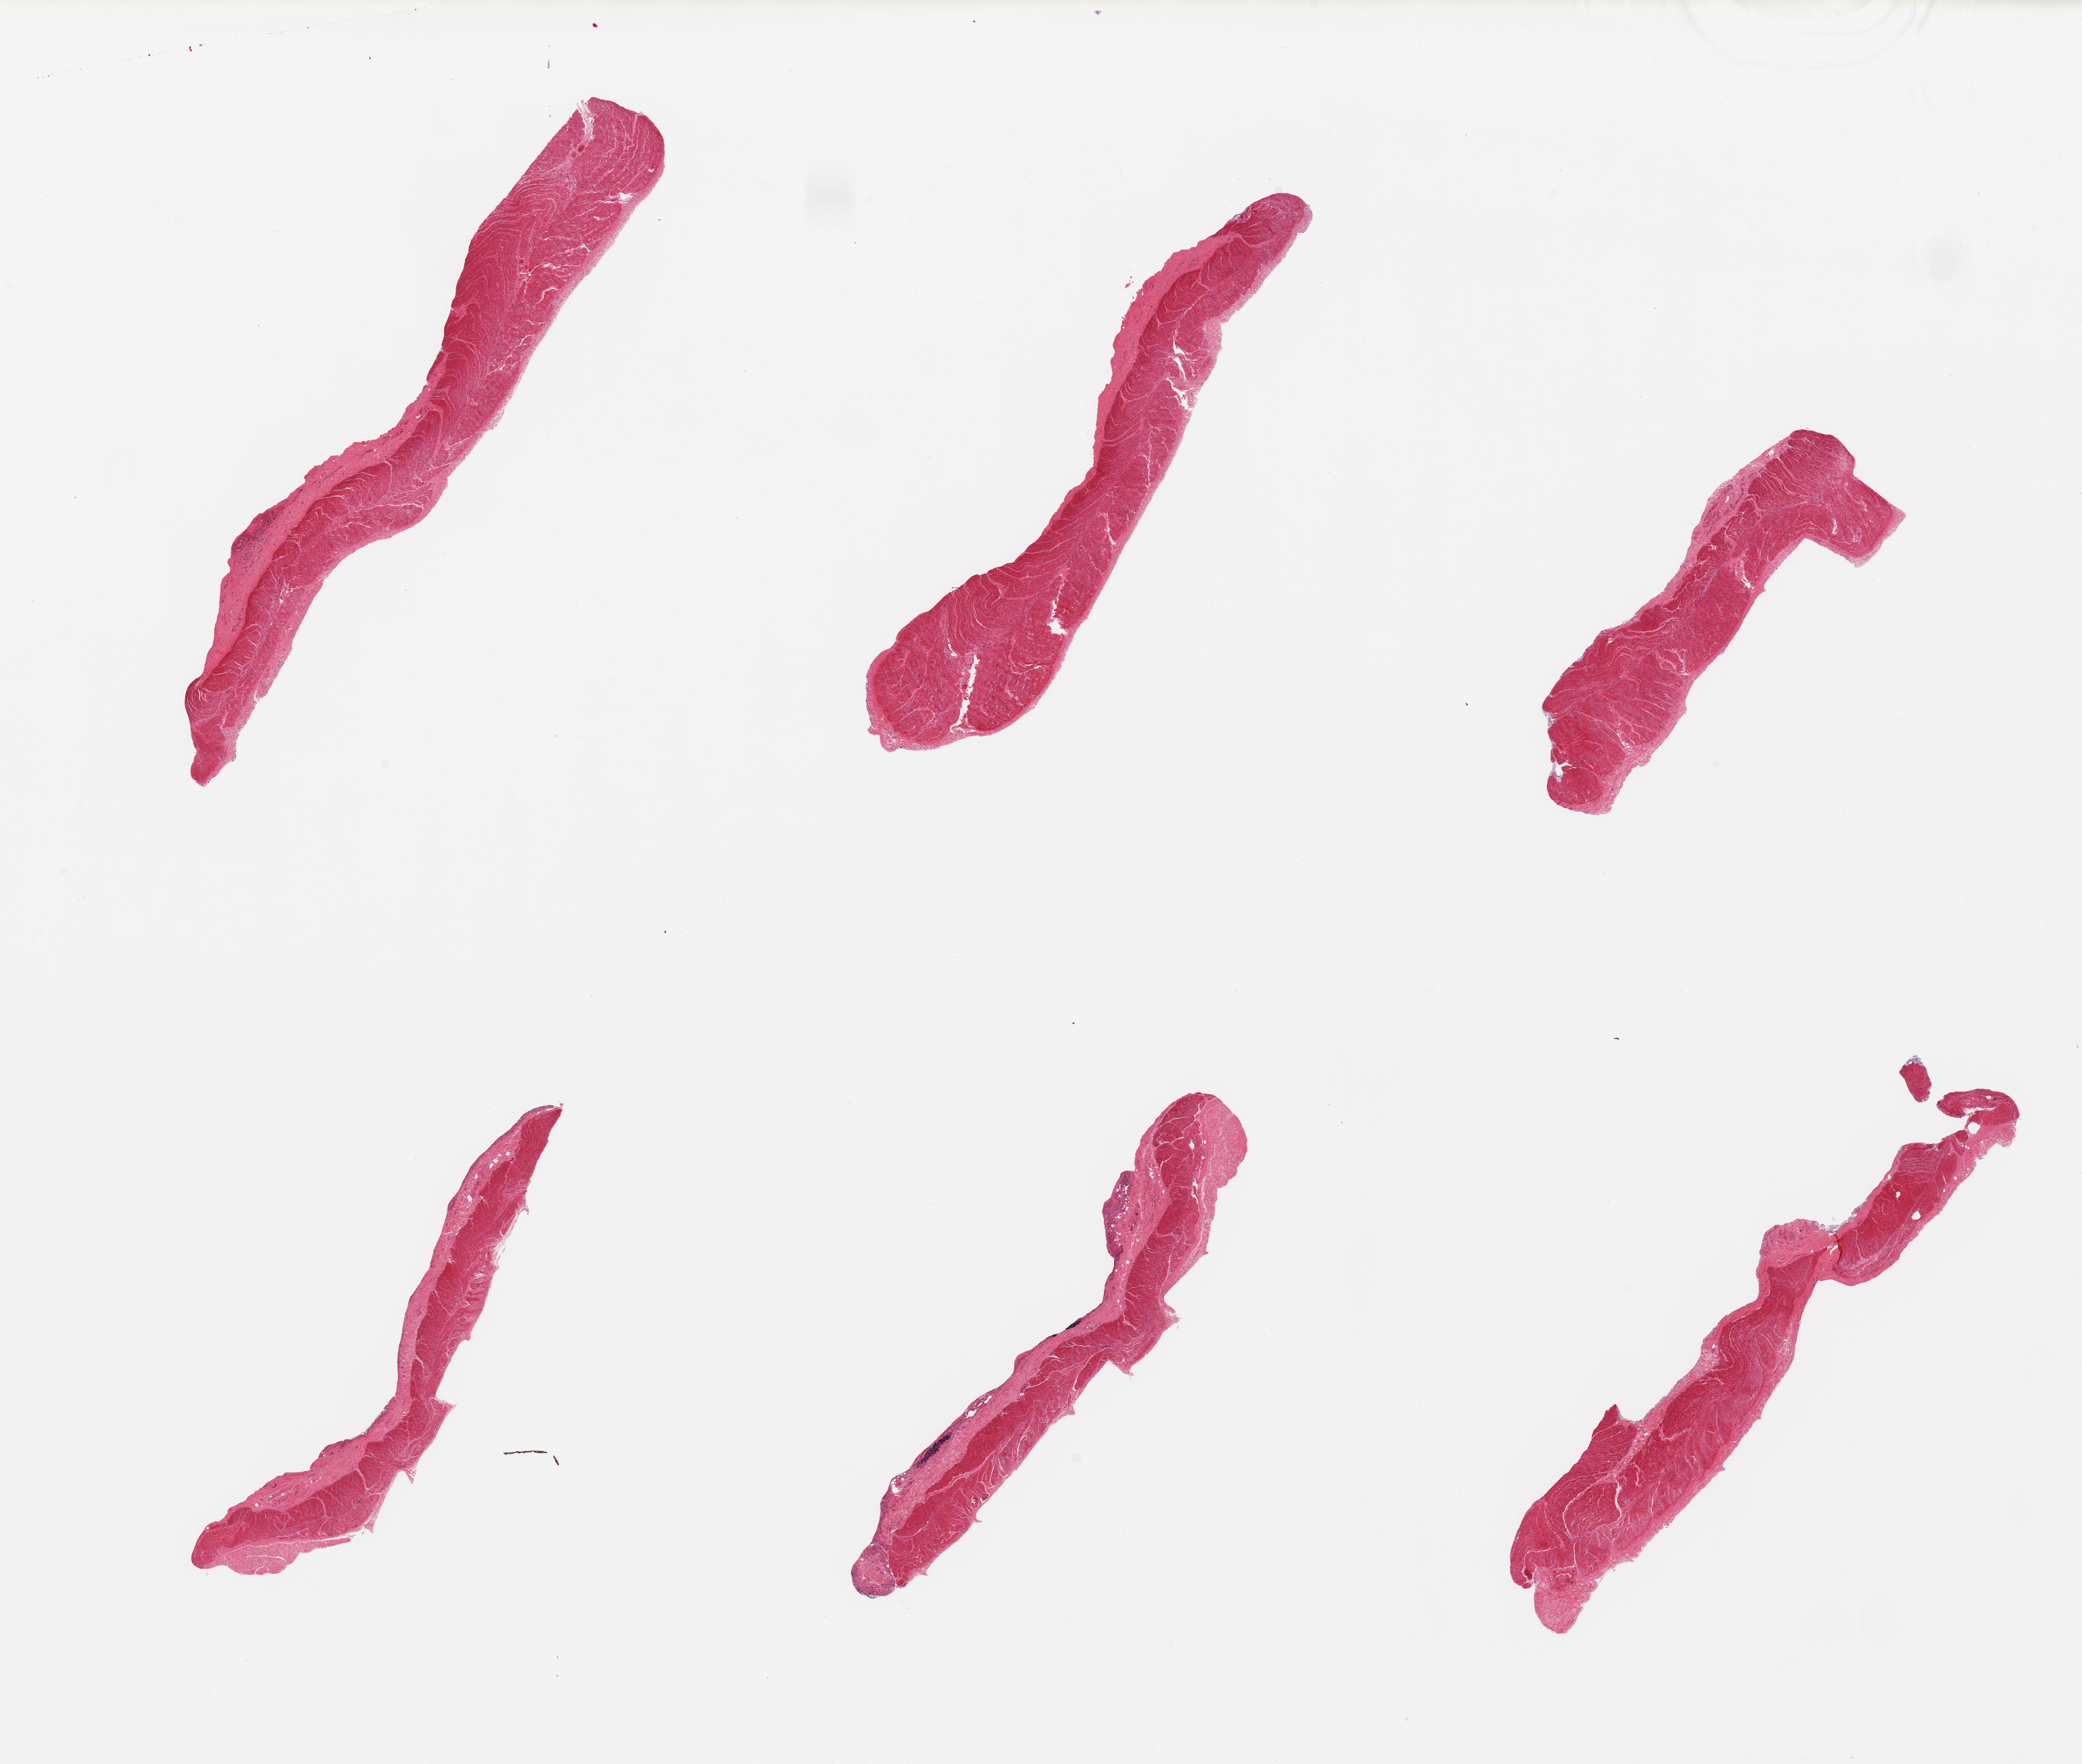
Digitized hematoxylin and eosin (H&E)-stained section, low-resolution overview of the scanned area, about 24.6 x 20.9 mm (slide scanned at 20x). PAXgene-fixed paraffin-embedded (PFPE) section. Section of sigmoid colon (target tissue). Tissue donor sample. Donor: male.
• pathologist's review note for this sample: 6 pieces; target muscularis, some residual submucosa and lymphoid aggregates